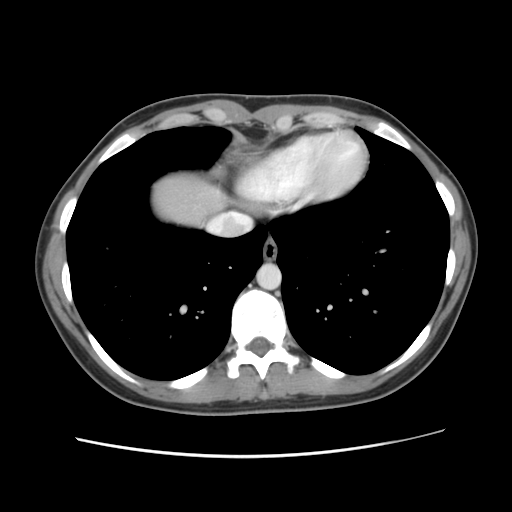
Contrast-enhanced abdominal CT, one axial slice; position 118 of 134 along the scan axis; 120 kVp; intravenous contrast given; soft-tissue window (W 400 / L 40 HU); 2.5 mm slice thickness; 512 × 512 image matrix, field of view 339 × 339 mm. Female patient, age 33 years. From the clinical record (not read from this slice): diagnosis: colorectal cancer liver metastases, imaged before liver resection; multiple liver metastases: yes; largest metastasis: 4.5 cm.
Outlined on this slice (expert manual segmentation):
- liver: box from (x=152, y=171) to (x=229, y=227) px
- planned liver remnant (the part of the liver to remain after resection): (x=152, y=172)–(x=228, y=227)